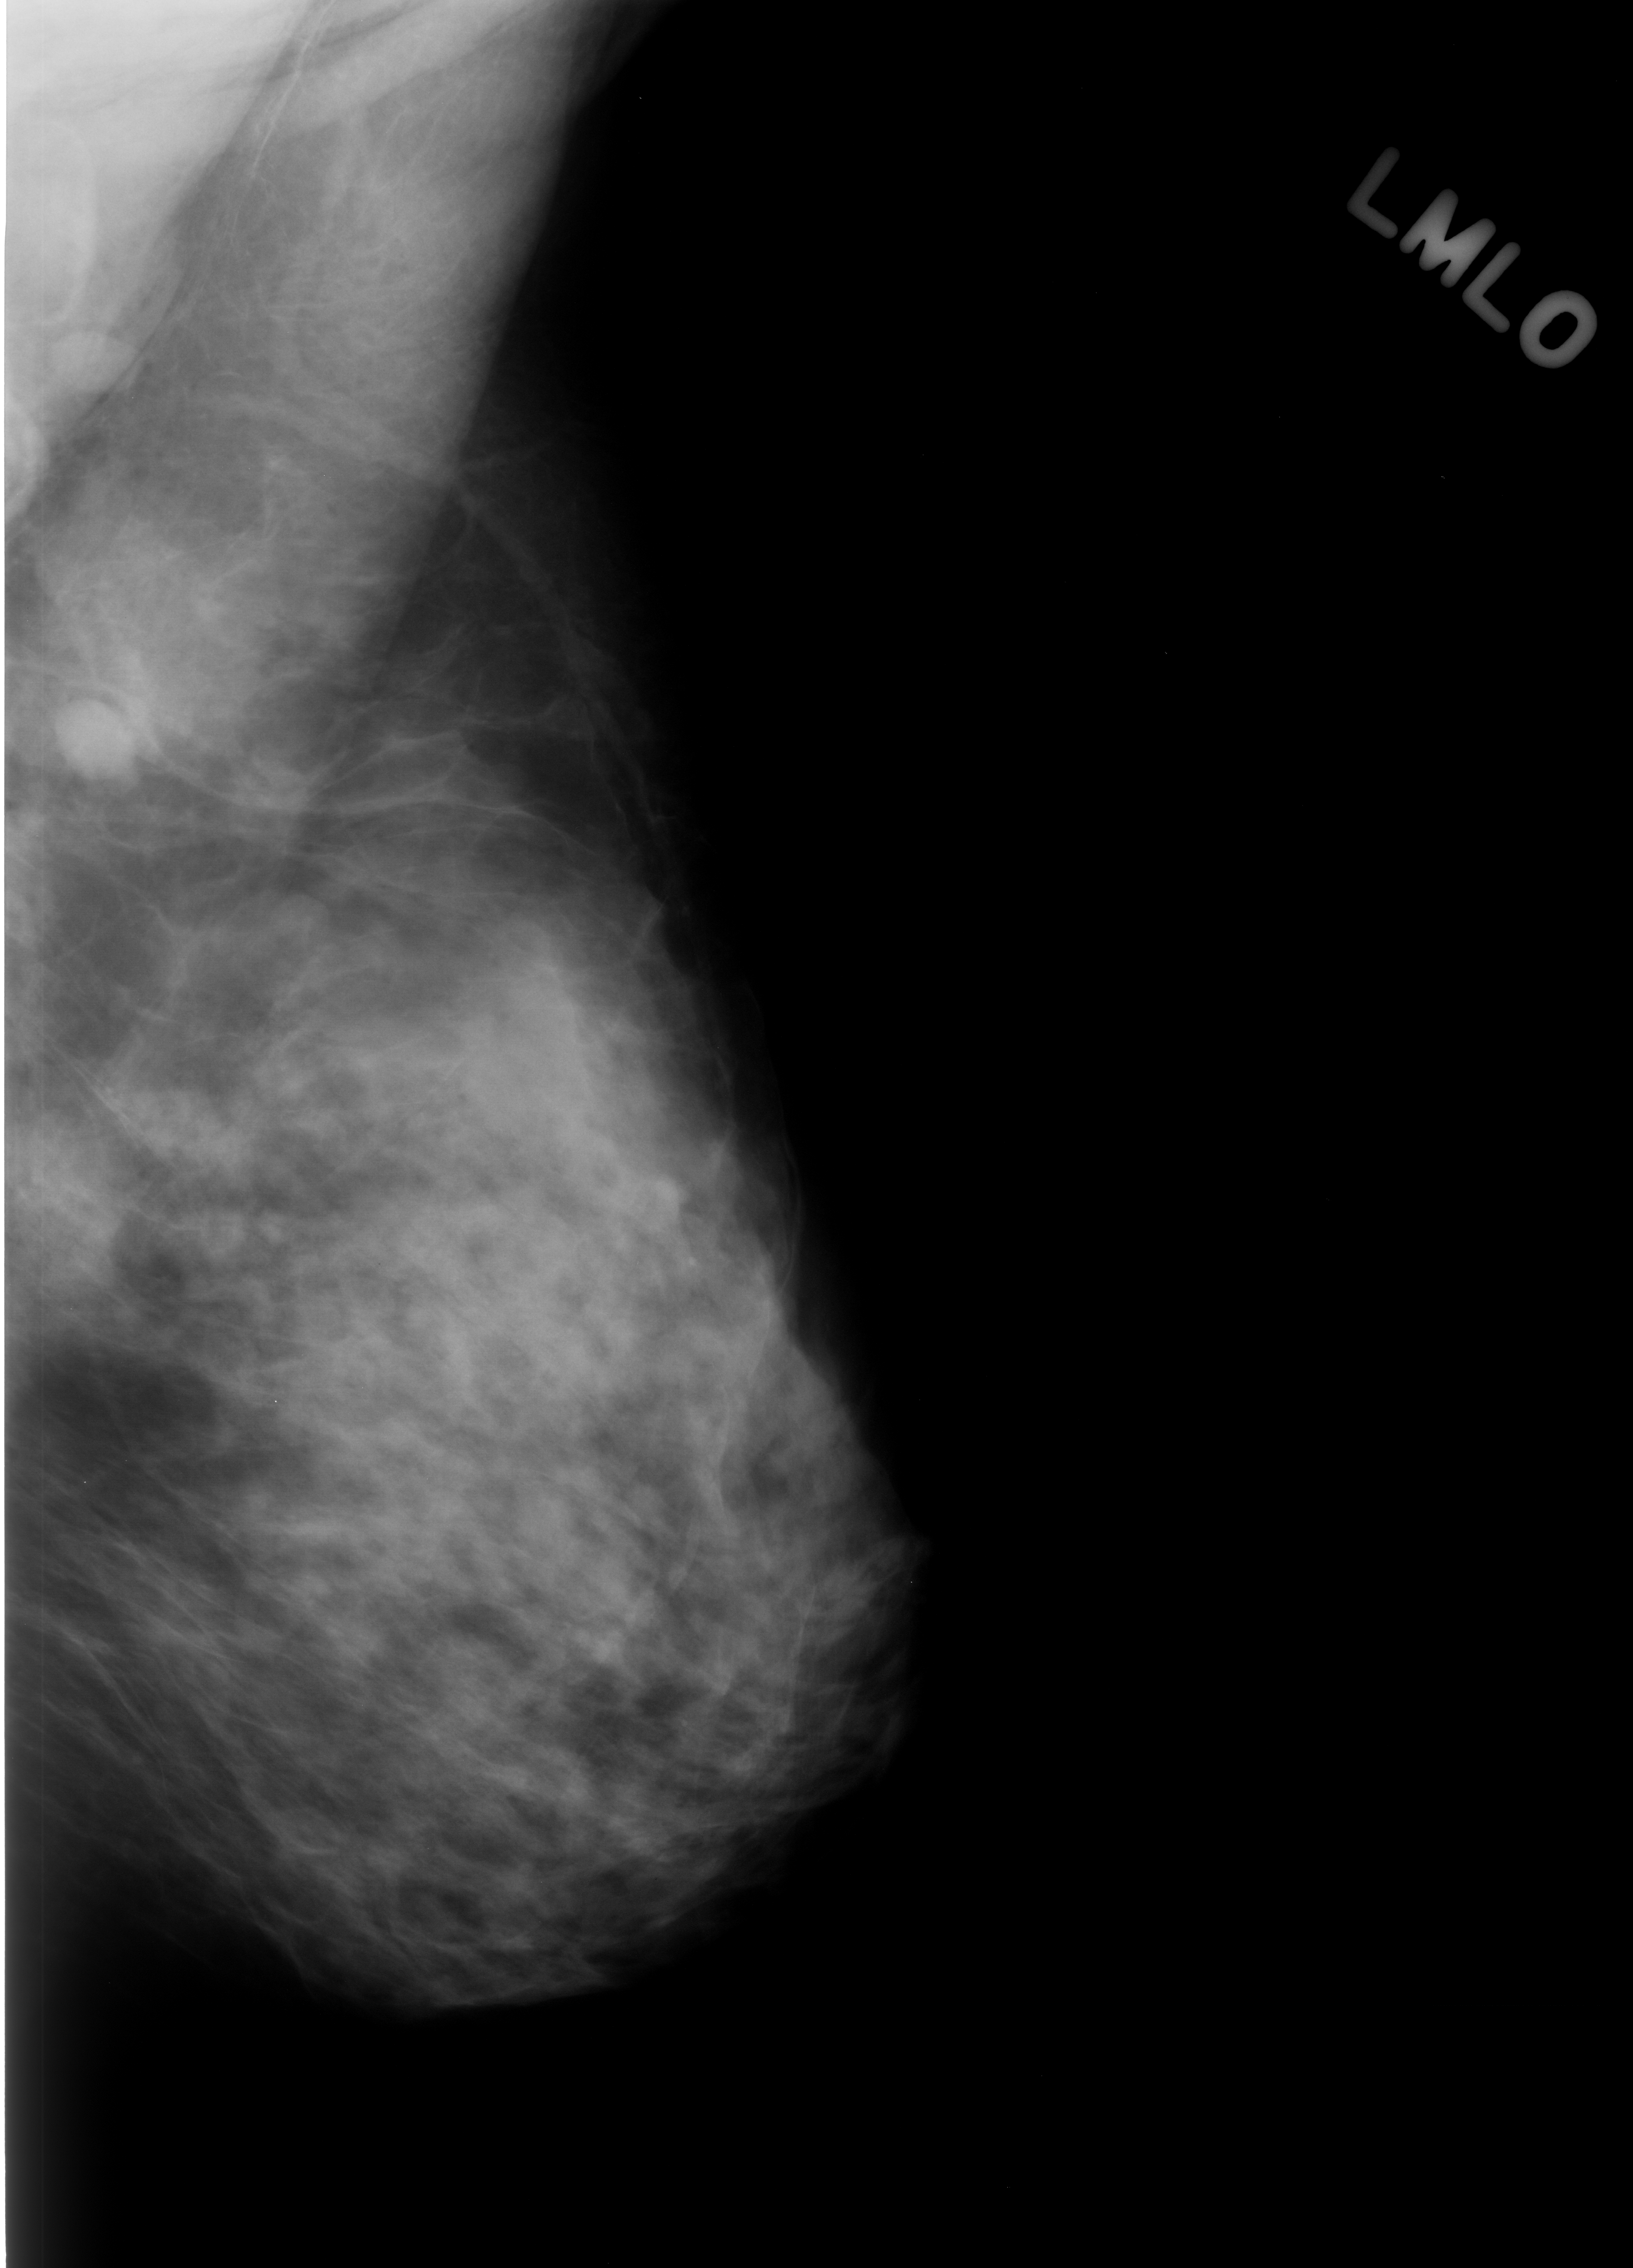
Digitized screen-film mammogram; left breast; MLO view; breast composition: heterogeneously dense (BI-RADS density category 3 of 4).
- Abnormality record for this image: Finding 1 of 2: mass, shape oval, margins circumscribed; BI-RADS assessment category 3; pathology result (as recorded, not read from the image): benign.
- Finding 2 of 2: mass, shape oval, margins circumscribed; BI-RADS assessment category 3; pathology (as recorded): benign.